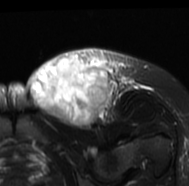
MRI of an extremity soft-tissue mass, one axial slice; slice 44 of 77 in the series (ordered by position); T2-weighted fat-saturated; MR volume resampled by the dataset authors to the PET/CT grid (not the native acquisition matrix); 189 × 186 image matrix, field of view 185 × 182 mm. Female patient. Case-level facts recorded for this patient, not image findings: histological type: leiomyosarcoma; grade: high; site of the primary tumour: groin.
Outlined on this slice (expert contour drawn on MRI and transferred to this co-registered scan by the dataset authors):
- gross tumour volume including surrounding oedema: box from (x=26, y=47) to (x=146, y=130) px
- gross tumour volume (mass): (x=28, y=54)–(x=112, y=128)